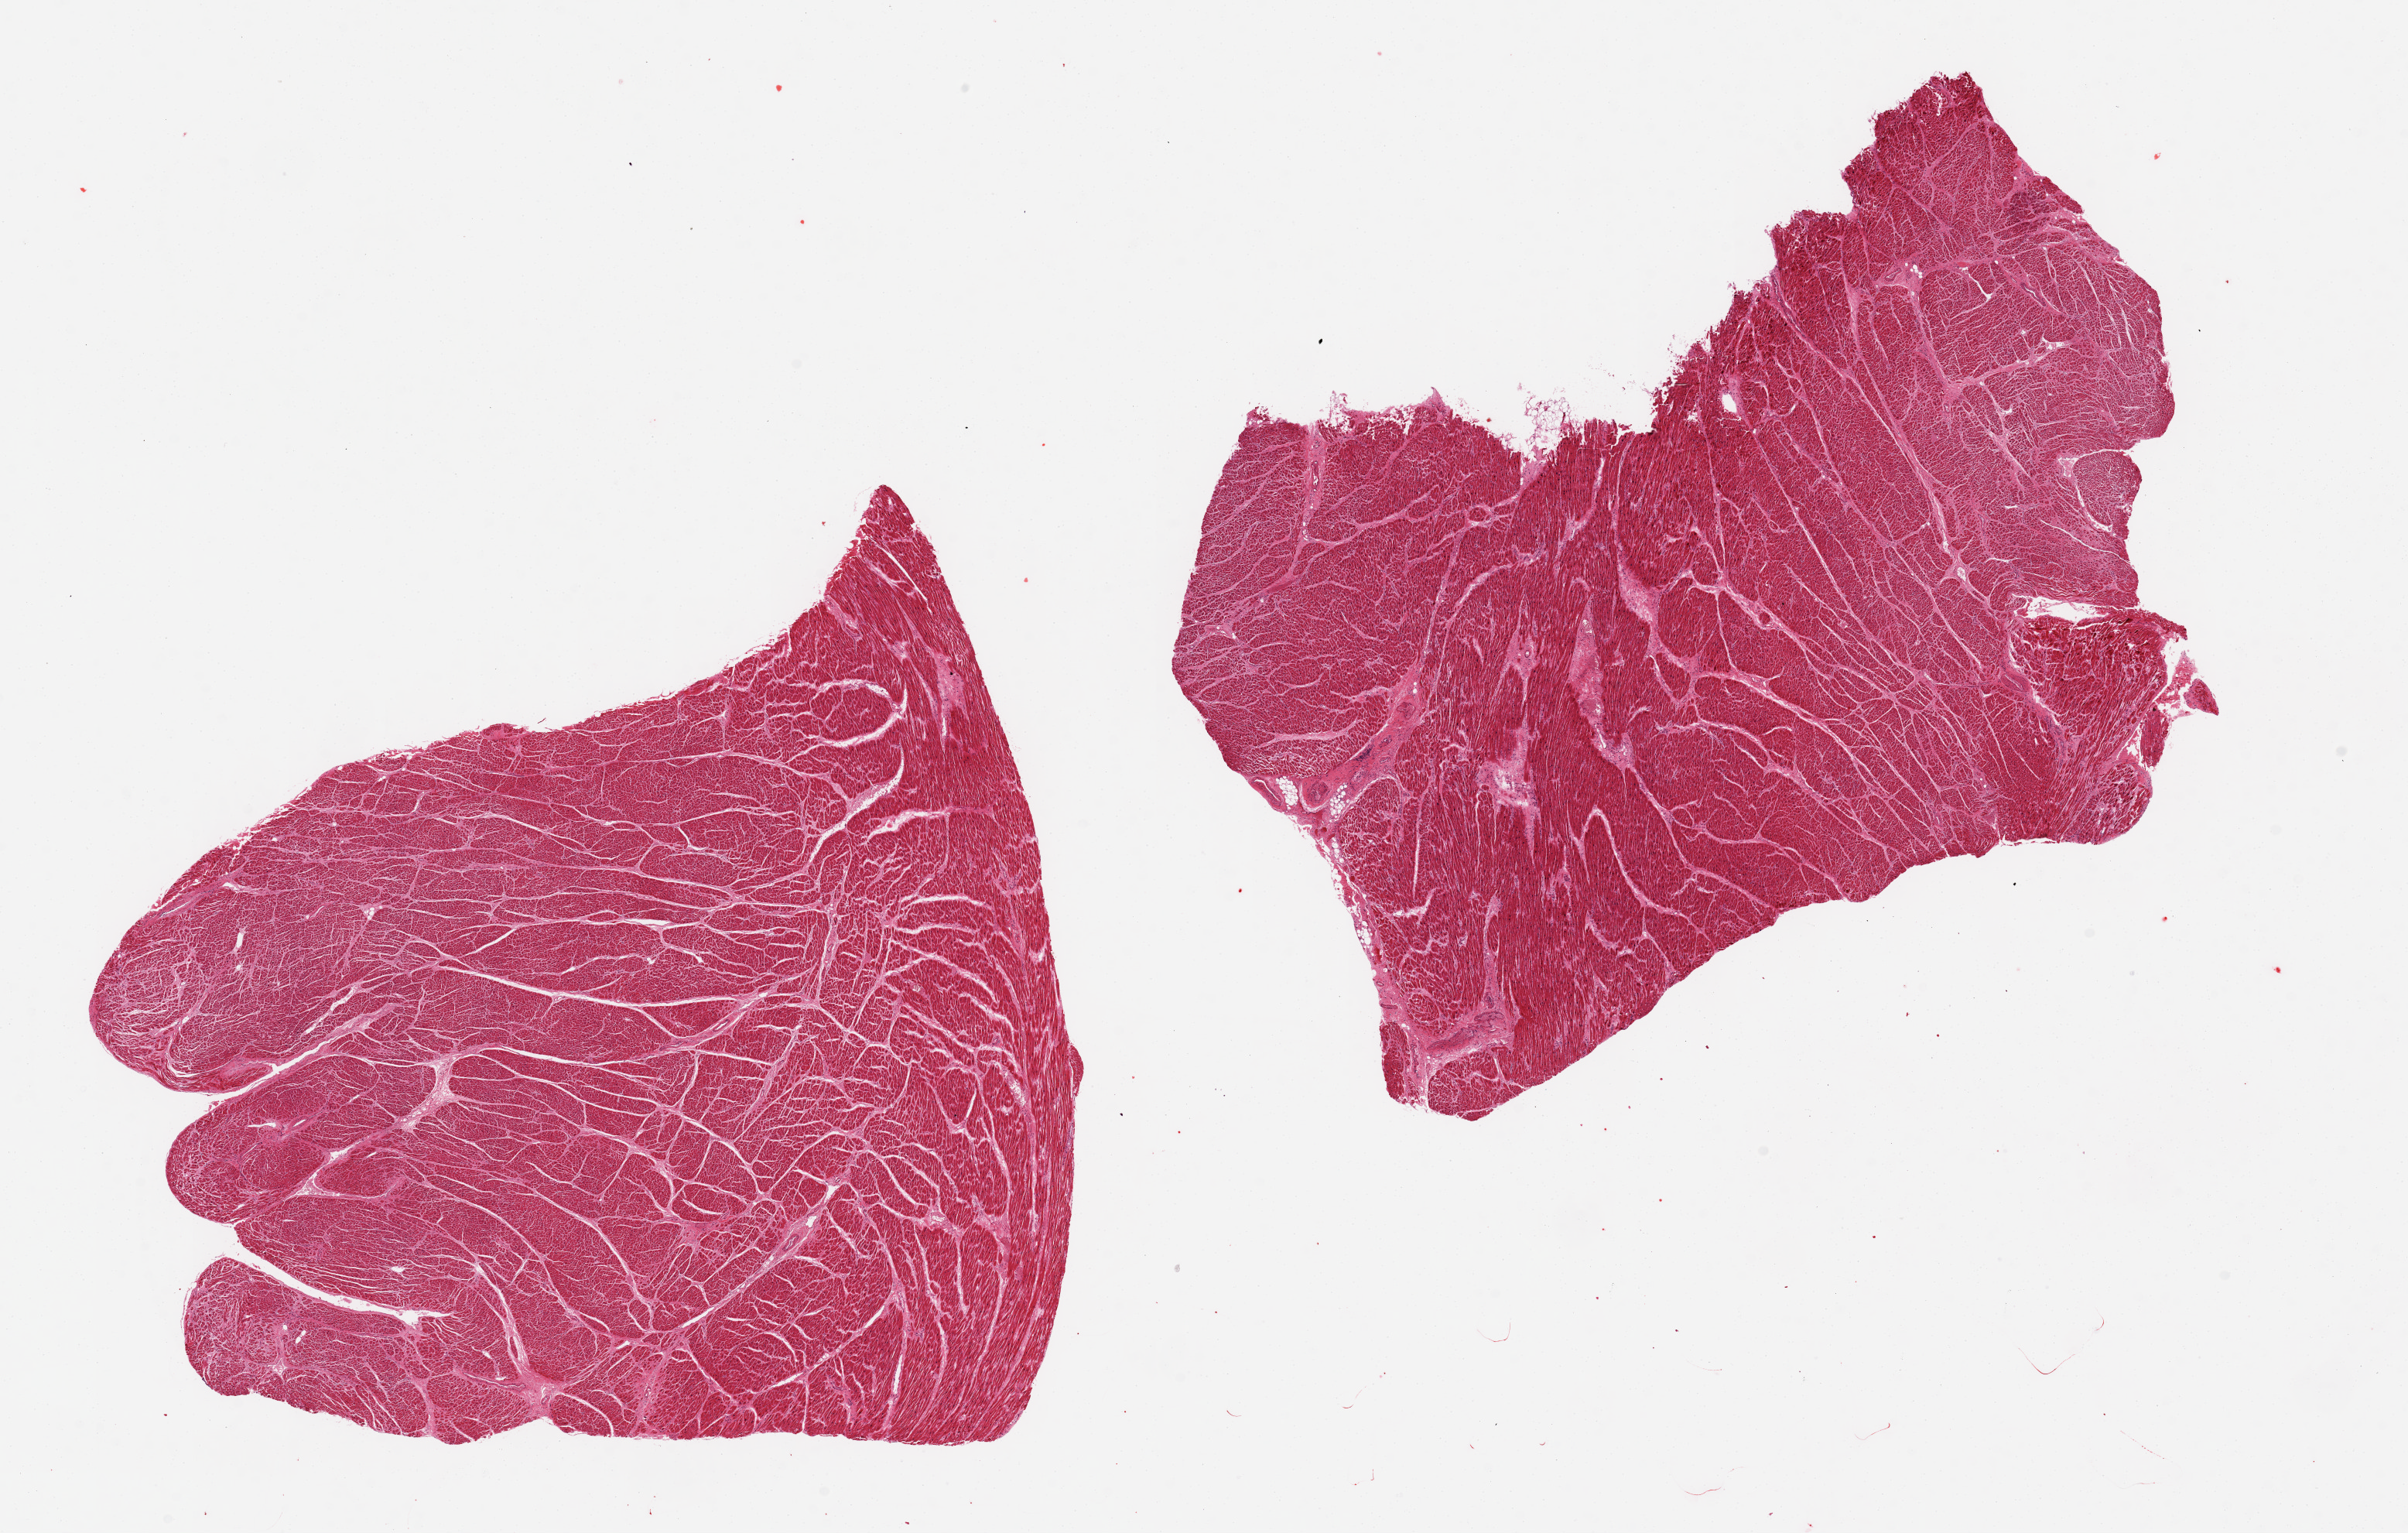
Whole-slide image, haematoxylin and eosin stain — whole scanned area (about 24.6 x 15.7 mm, from a 20x scan) shown as a low-resolution overview. PAXgene-fixed, paraffin-embedded tissue. Sampled site (target tissue): heart. Tissue donor sample. Donor: female.
Pathologist's review note for this sample: 2 pieces, 10x9 & 10x7 mm; slight to moderate interstitial fibrosis; no inflammation or obvious infarction.